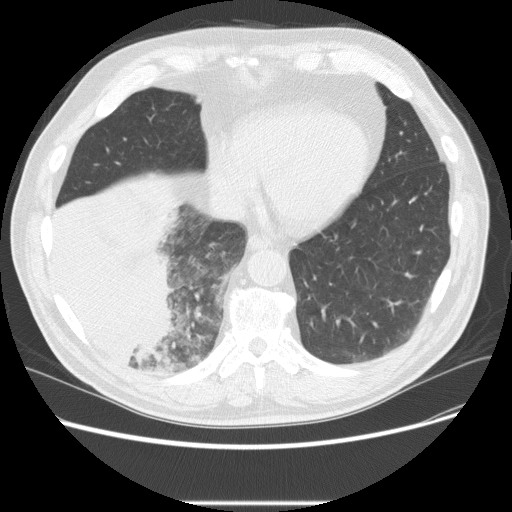
Low-dose screening chest CT, one axial slice. Slice 67 of 233 in the series (ordered by position). Reconstruction kernel STANDARD. 120 kVp. Lung window (W 1500 / L -600 HU). 2.5 mm slice thickness. 512 × 512 image matrix, field of view 380 × 380 mm.
Outlined on this slice (manually delineated by an expert):
- lesion 3 (tumor, lower lobe of right lung): bounding box [x1, y1, x2, y2] px = [51, 196, 177, 366]